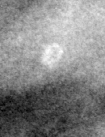
Region of interest cut from a scanned film mammogram (one marked finding), right breast, MLO view.
Calcifications, morphology lucent centered; BI-RADS assessment category 2; subtlety rating 3 on a 1 (subtle) to 5 (obvious) scale; benign without callback (not worked up further).